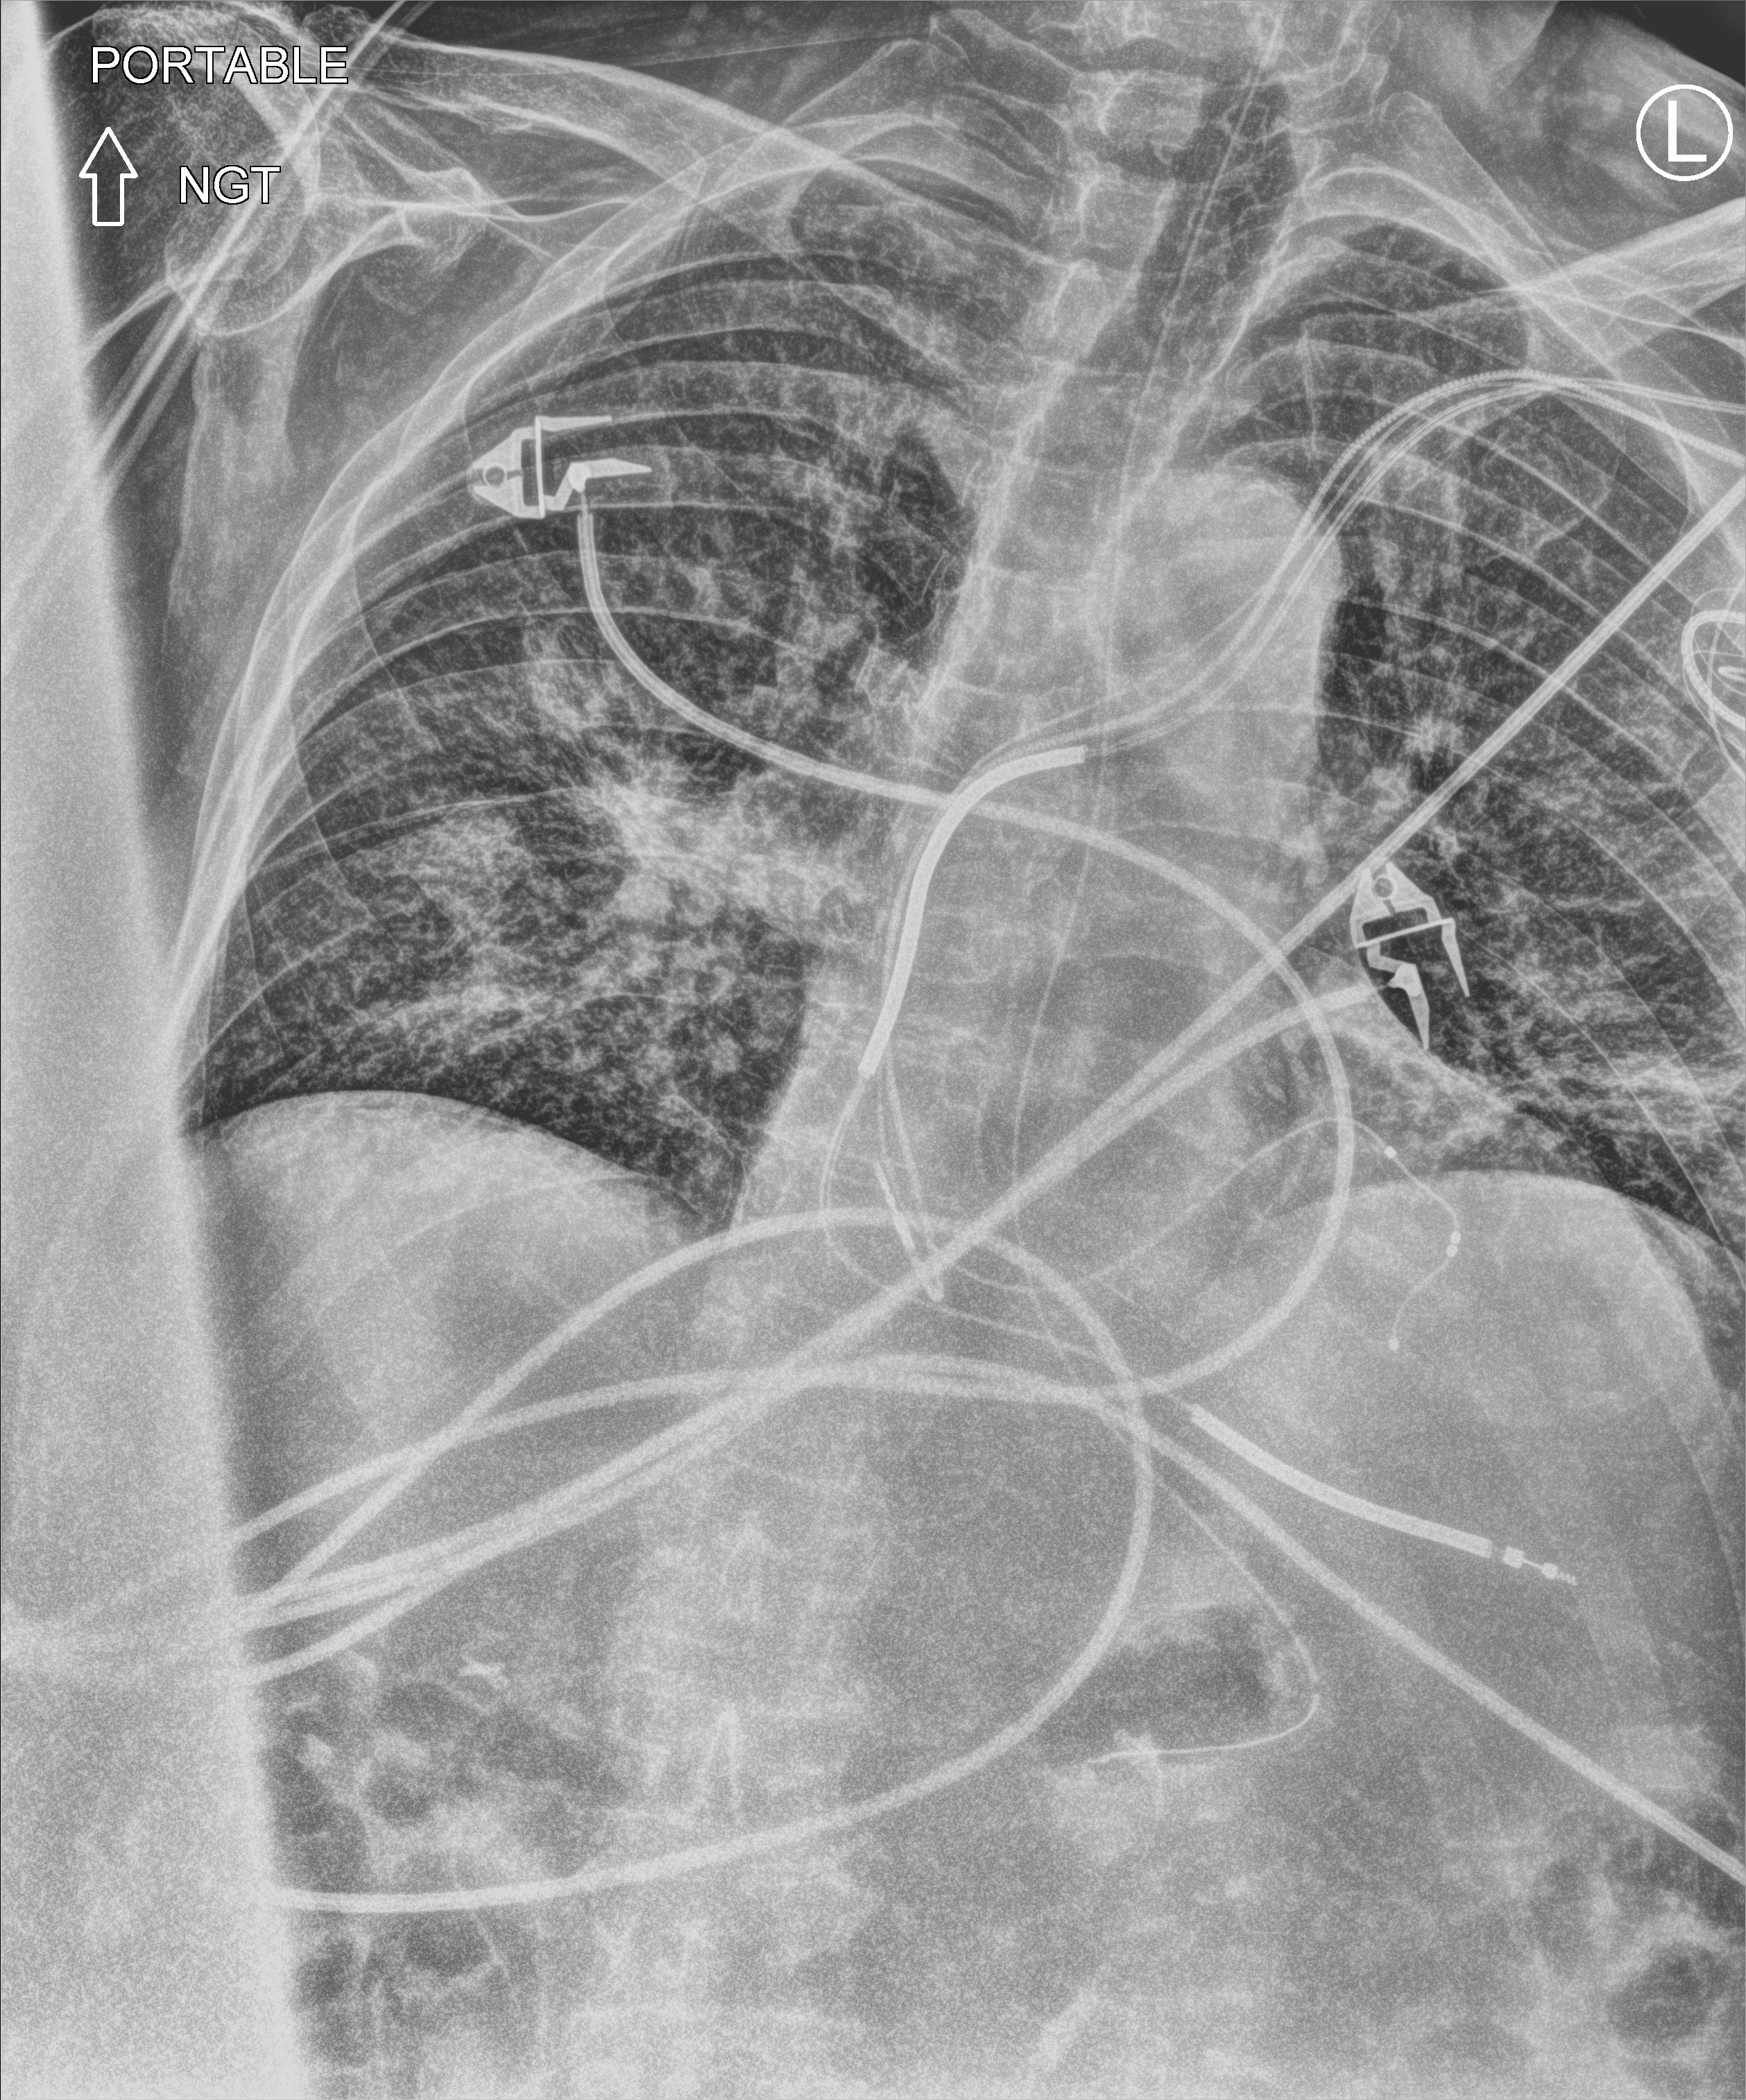
Chest X-ray (portable). Male patient hospitalised with COVID-19, age 75–90 years.
From the hospital-stay record, not from the radiograph (when in the stay this image was taken is not recorded):
- admitted to intensive care during this hospital stay: no